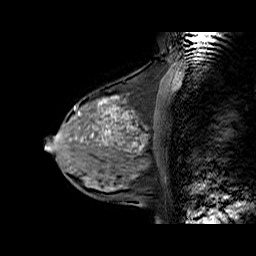
Breast MRI (dynamic contrast-enhanced), one sagittal slice; position 25 of 60 along the scan axis; dynamic contrast-enhanced series, time point 2 of 6 at this slice position (early post-contrast); 1.5 T; TE 6.3 ms, TR 32.9 ms; 256 × 256 image matrix. Female patient. Case-level facts recorded for this patient, not image findings: setting: breast cancer imaged before/during neoadjuvant chemotherapy; receptor status: HR-positive, HER2-negative.
Annotated regions visible in this slice (semi-automatically segmented with operator editing):
- analysis volume of interest (the breast-tissue region the enhancement analysis was run in; not a lesion): bounding box (x1, y1, x2, y2) in pixels: (57, 86, 169, 170)
- tumour enhancement mask (voxels above the 100 % enhancement threshold inside the analysis volume of interest): (78, 97, 129, 136)